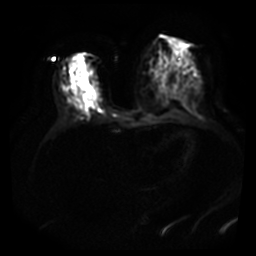
Breast MRI, one axial slice. Position 19 of 40 along the scan axis. Diffusion-weighted series; image 2 of 4 stored at this slice position (different b-values; order by instance number). 3 T. 256 × 256 image matrix, field of view 380 × 380 mm. Female patient.
Annotated regions visible in this slice (manually delineated by an expert):
- tumour on diffusion-weighted imaging: box from (x=82, y=94) to (x=87, y=101) px